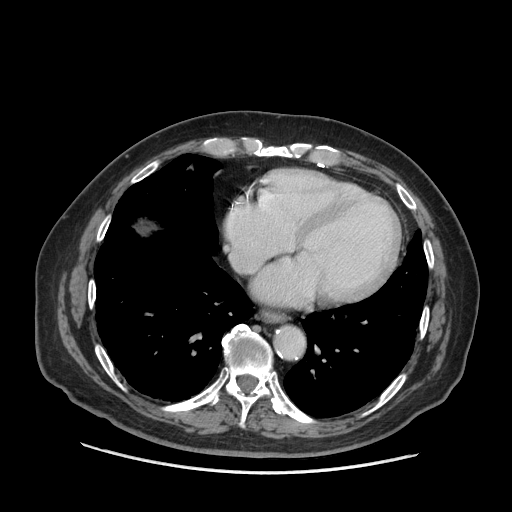
Contrast-enhanced abdominal CT (liver protocol), one axial slice; slice 69 of 77 in the series (ordered by position); reconstruction kernel STANDARD; 140 kVp; soft-tissue window (W 400 / L 40 HU); 2.5 mm slice thickness; 512 × 512 image matrix, field of view 420 × 420 mm. From the clinical record (not read from this slice): diagnosis: hepatocellular carcinoma (patient treated with transarterial chemoembolisation; whether this scan precedes or follows treatment is not stated here); TNM stage (as recorded): Stage-I; Child-Pugh class: A; tumour differentiation: well differentiated; tumour nodularity: uninodular.
Outlined on this slice (semi-automatic segmentation, software-assisted and operator-edited):
- liver parenchyma outside the tumour (the mass and vessels are separate outlines, so this box may not span the whole liver): bounding box <140,226,148,232> (left, top, right, bottom; pixels)